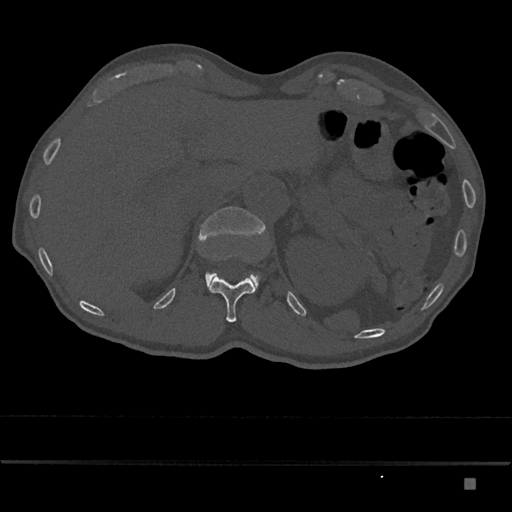
CT including the spine, one axial slice. Slice 589 of 797 in the series (ordered by position). Reconstruction kernel Br40s/3. Bone window (W 1800 / L 400 HU). 512 × 512 image matrix, field of view 390 × 390 mm. Male patient, age 72 years. From the clinical record (not read from this slice): primary cancer: prostate.
Annotated regions visible in this slice (semi-automatically segmented with operator editing):
- L1 vertebra: bounding box (x1, y1, x2, y2) in pixels: (198, 207, 266, 291)
- T12 vertebra: (209, 276, 255, 322)